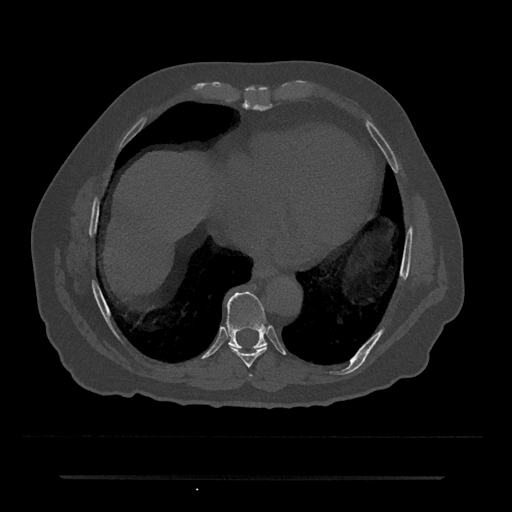
CT including the spine, one axial slice; position 307 of 797 along the scan axis; reconstruction kernel Br40s/3; 120 kVp; bone window (W 1800 / L 400 HU); 0.5 mm slice thickness; 512 × 512 image matrix, field of view 437 × 437 mm. Patient: male, 69 years. Case-level facts recorded for this patient, not image findings: primary cancer: prostate.
Structures marked on this image (semi-automatically segmented with operator editing):
- T8 vertebra: box from (x=229, y=345) to (x=267, y=367) px
- T9 vertebra: (x=227, y=291)–(x=267, y=349)